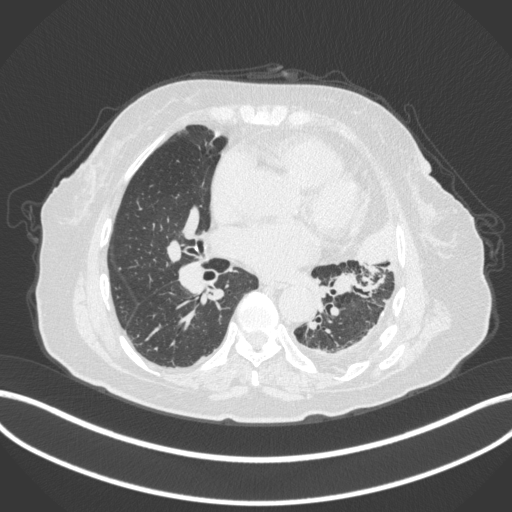
Chest CT, one axial slice; slice 175 of 399 in the series (ordered by position); 120 kVp; lung window (W 1500 / L -600 HU); 1 mm slice thickness; 512 × 512 image matrix, field of view 400 × 400 mm. Patient: female, 75 years. From the clinical record (not read from this slice): clinical TNM (as recorded): T3 N3 M1.
Annotated regions visible in this slice (rectangle marked by the reading radiologist):
- lung tumour (recorded histology: adenocarcinoma): box from (x=355, y=214) to (x=401, y=269) px